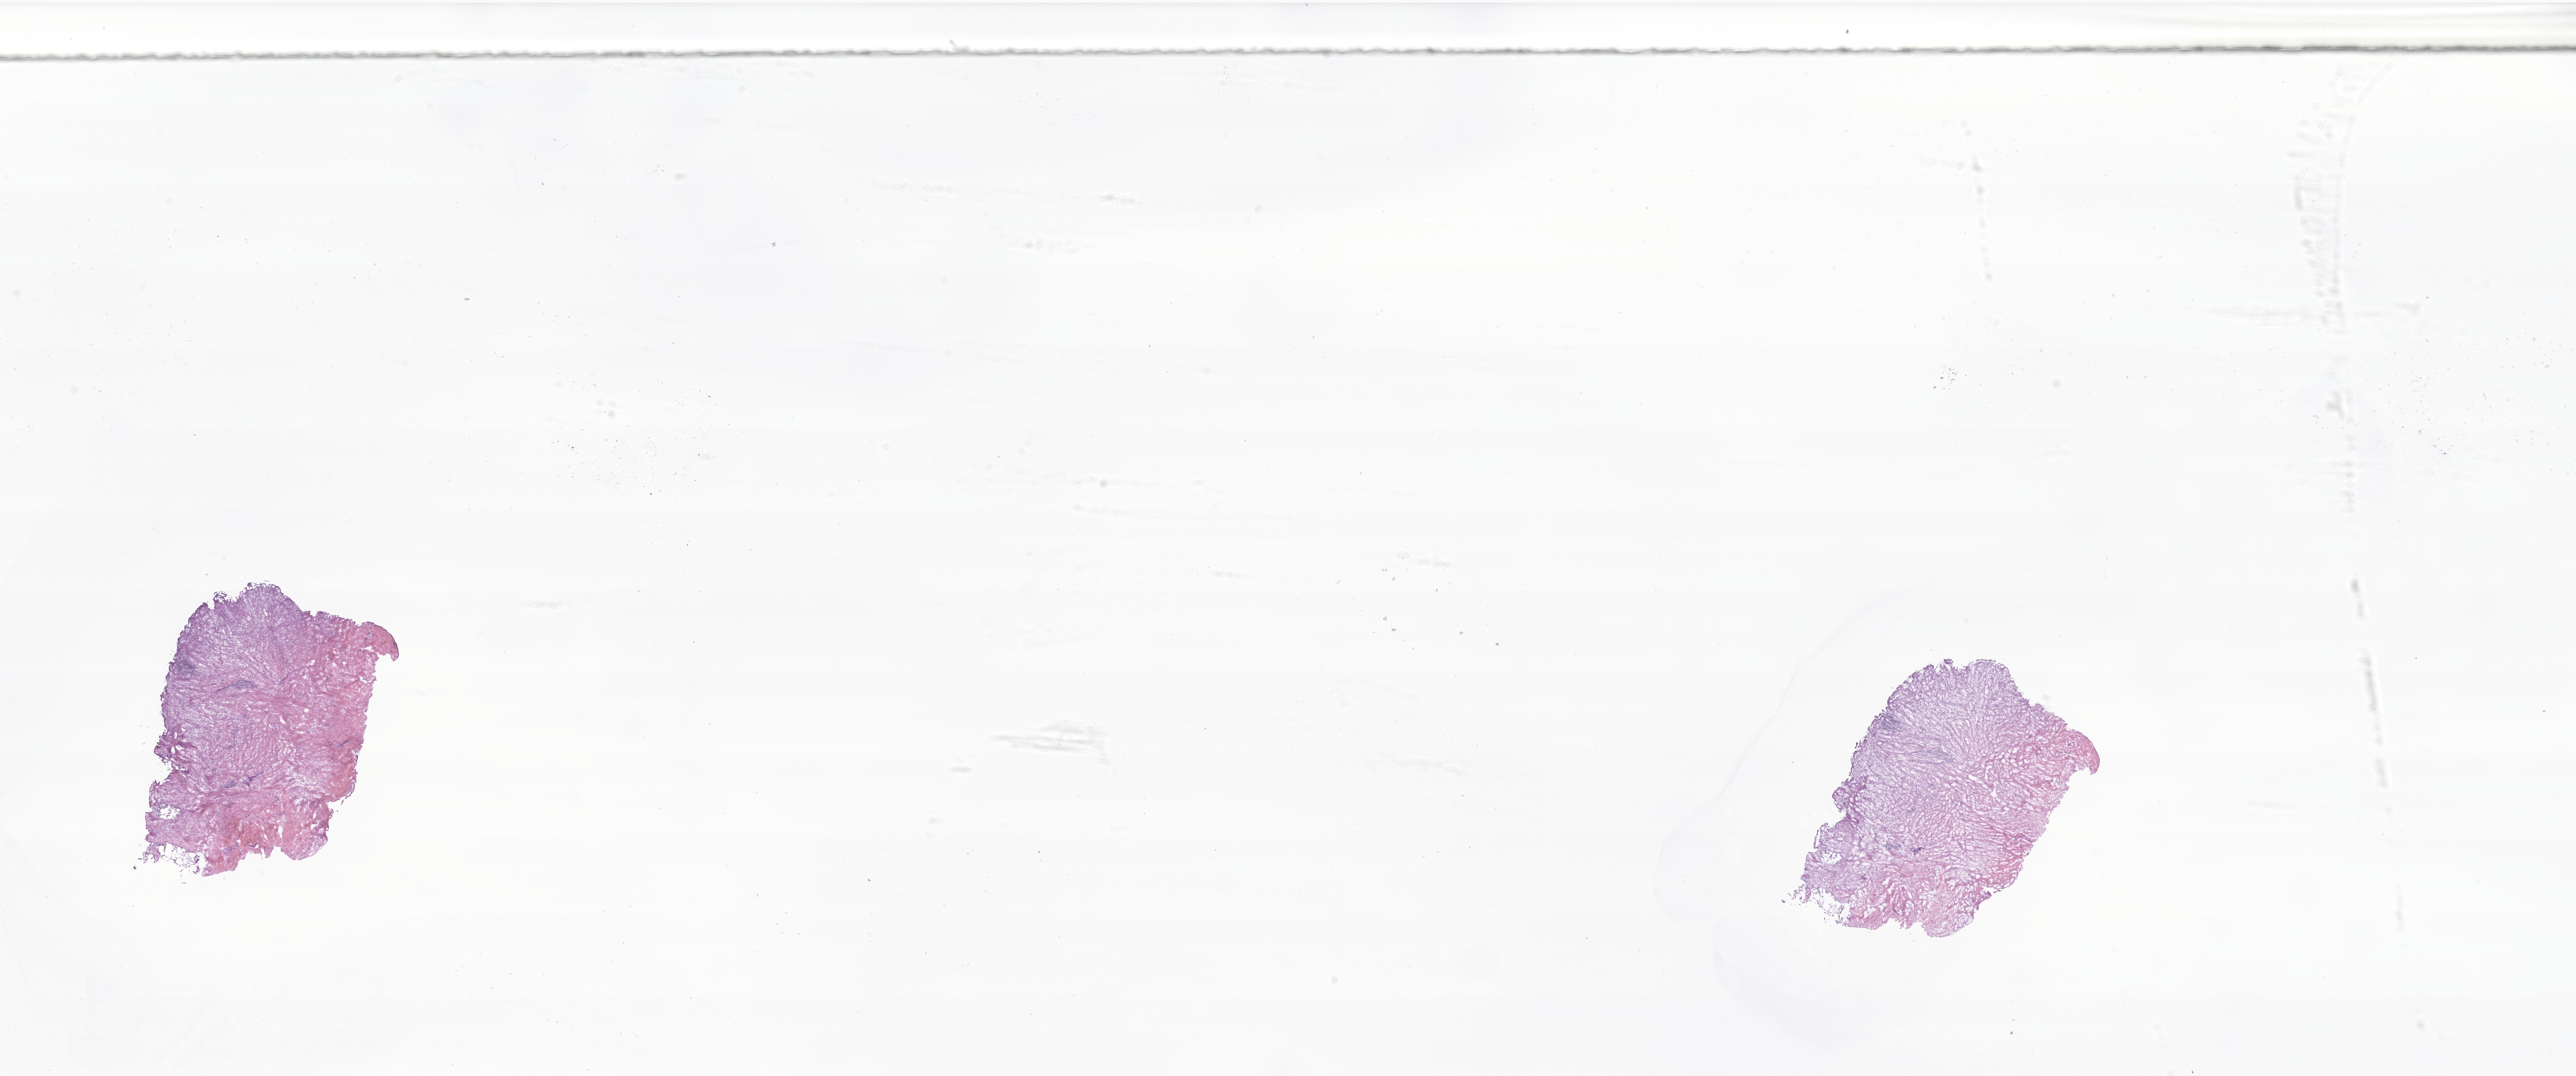
Digitized H&E-stained section of tumor tissue from the soft tissue of abdomen — a low-resolution overview of the entire scanned area, about 33.8 x 14.1 mm. Frozen section. Patient: female, age 207 months (17 years 3 months).
Recorded diagnosis: Aggressive fibromatosis.